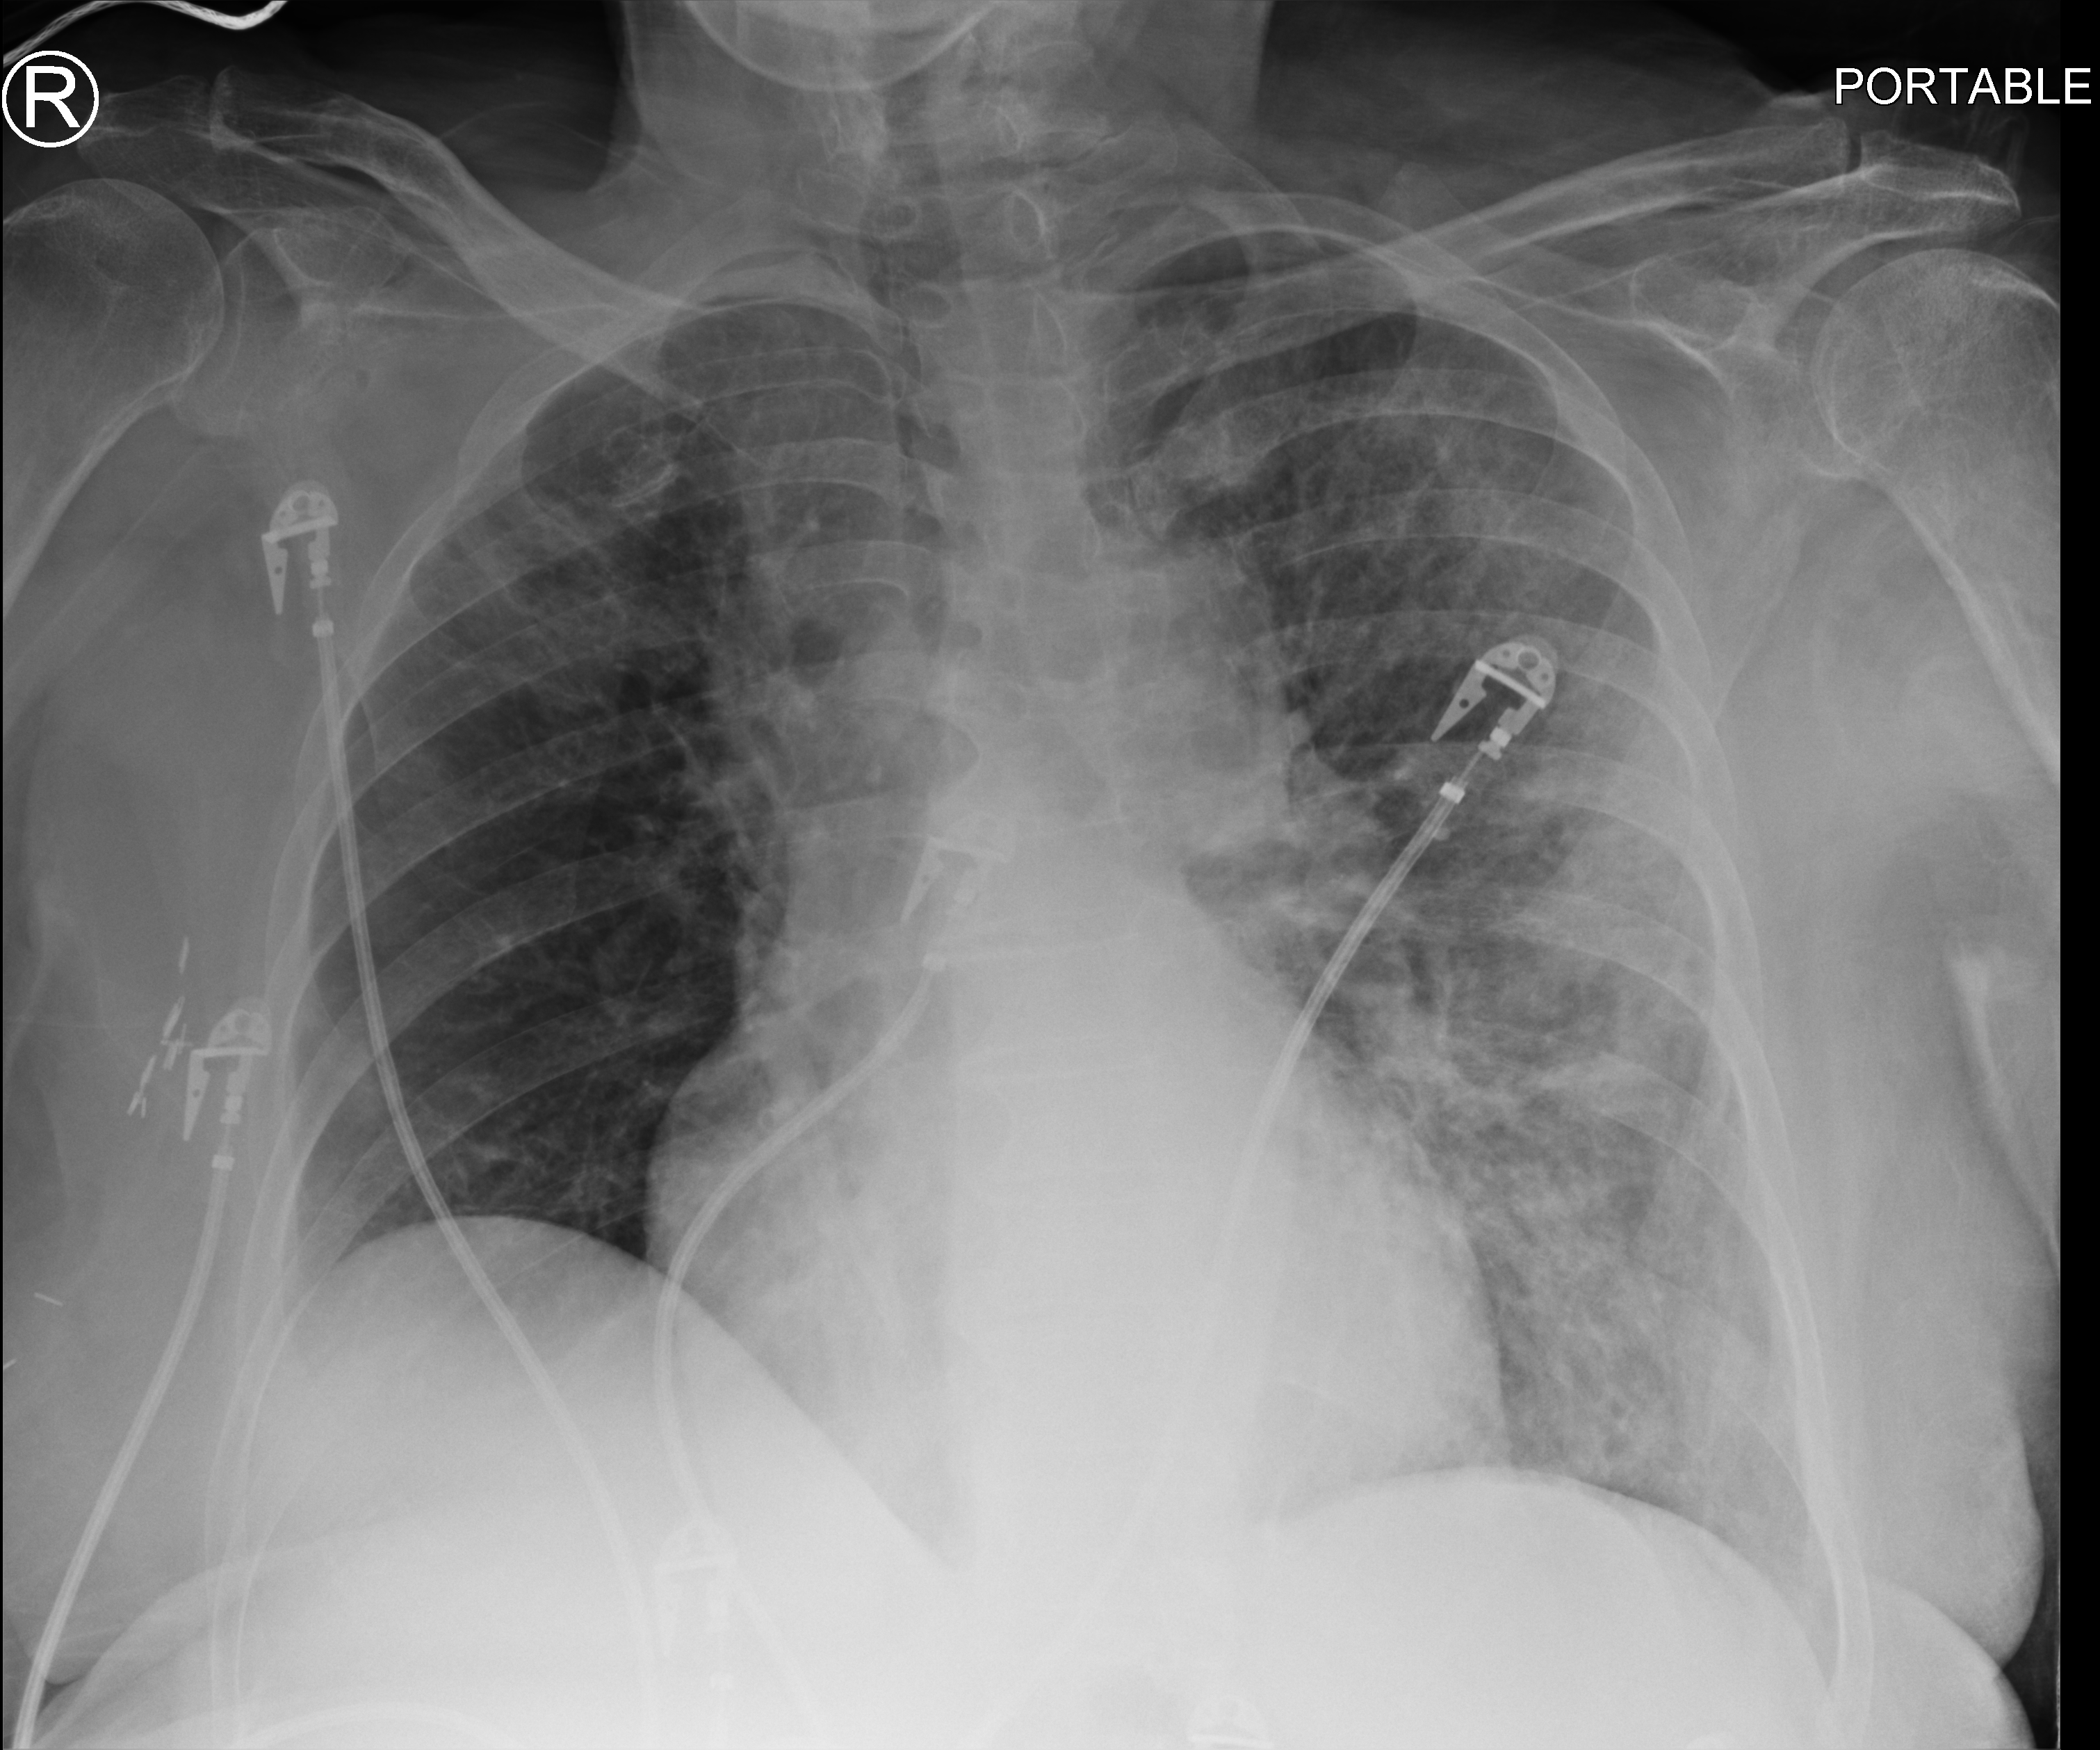
Chest X-ray (portable). Patient hospitalised with COVID-19; female, aged 60–74 years.
Hospital-stay facts (about this admission, not read from this image; timing relative to this image not recorded):
- diabetes (admission record): no
- length of hospital stay: 12 days
- mechanically ventilated during this hospital stay: no